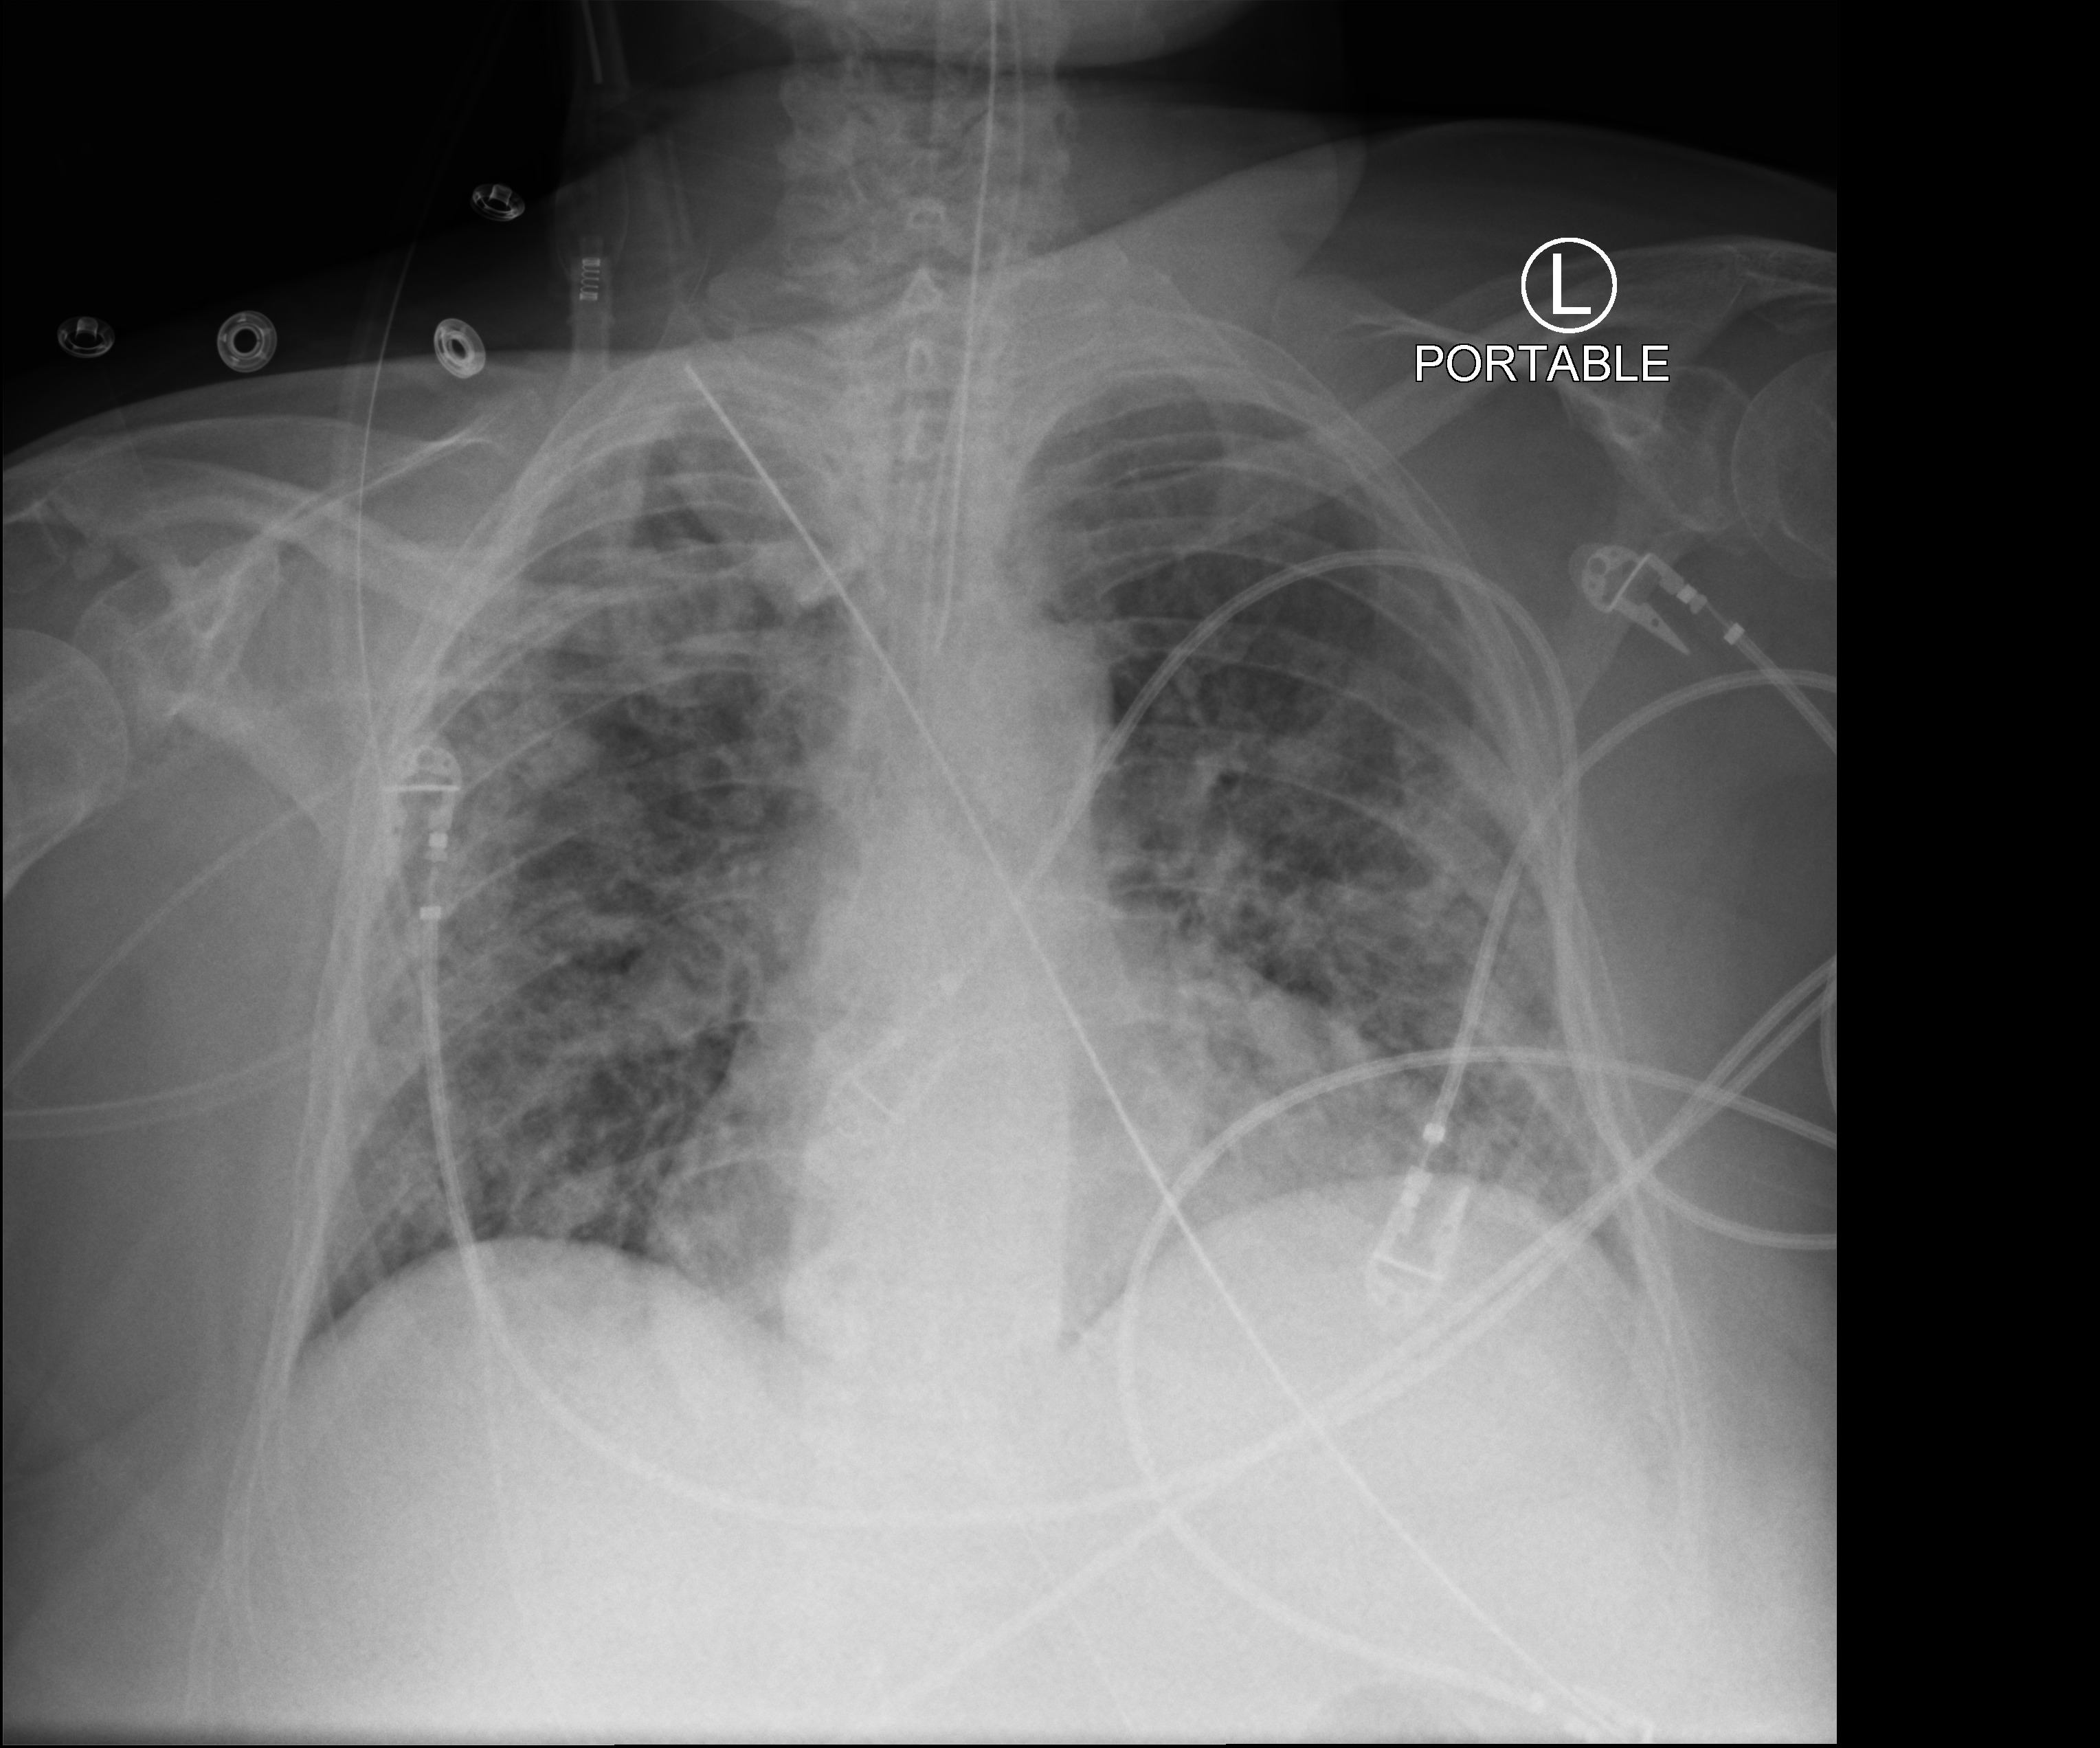
Portable chest radiograph. Patient hospitalised with COVID-19; female, aged 75–90 years.
Hospital-stay facts (about this admission, not read from this image; timing relative to this image not recorded):
- hypertension (admission record): yes
- smoking status (admission record): former